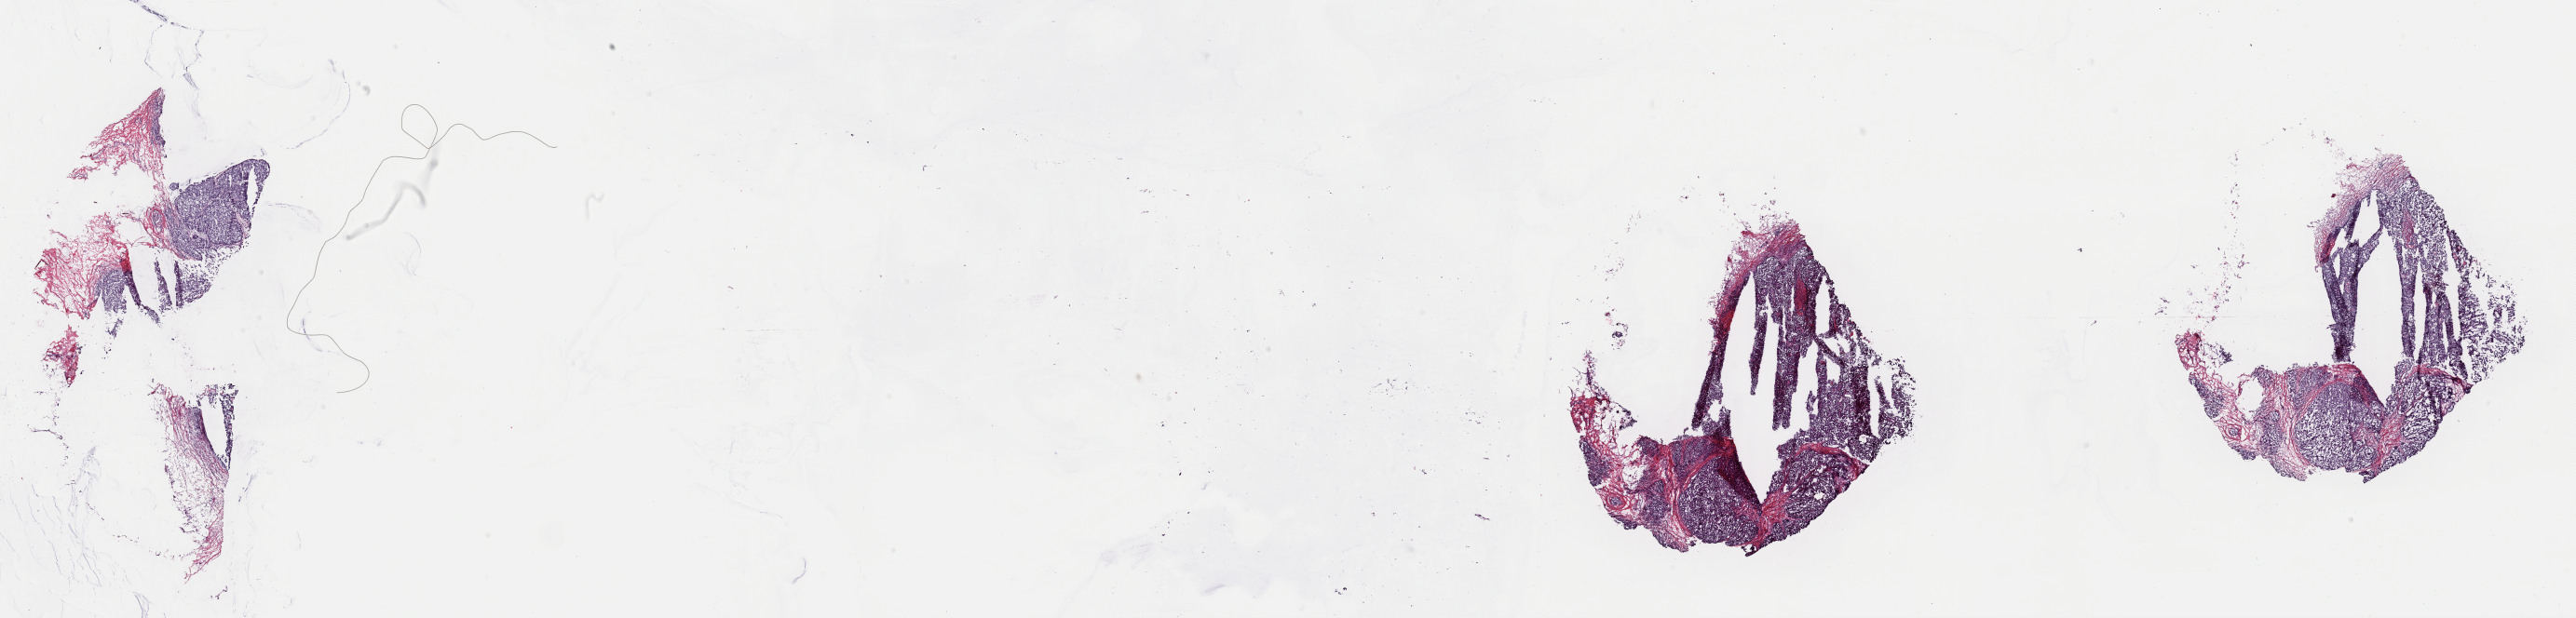
Digitized Hematoxylin and eosin (H&E) stained tissue section (whole slide) — low-resolution overview of the scanned area, about 43.7 x 10.5 mm (slide scanned at 40x); frozen section; primary tumour sample from the breast. Patient: female, age at initial diagnosis 66 years. Slide review estimates, as recorded: tumour cells 80%, tumour nuclei 80%, normal cells 1%, stromal cells 19%, necrosis 0%. Inflammatory infiltration, as recorded: lymphocyte infiltration 4%, monocyte infiltration 1%, neutrophil infiltration 1%.
Diagnosis: Papillary carcinoma, NOS. Laterality: right. AJCC pathologic stage: IIA (7th edition).